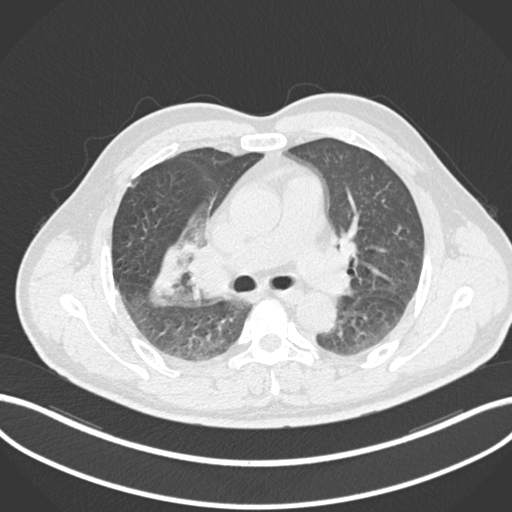
Chest CT, one axial slice; slice 638 of 852 in the series (ordered by position); 120 kVp; lung window (W 1500 / L -600 HU); 512 × 512 image matrix, field of view 400 × 400 mm. Male patient, age 55 years. Case-level facts recorded for this patient, not image findings: clinical TNM (as recorded): T3 N2 M1.
Outlined on this slice (rectangle marked by the reading radiologist):
- lung tumour (recorded histology: adenocarcinoma): box from (x=151, y=242) to (x=183, y=306) px